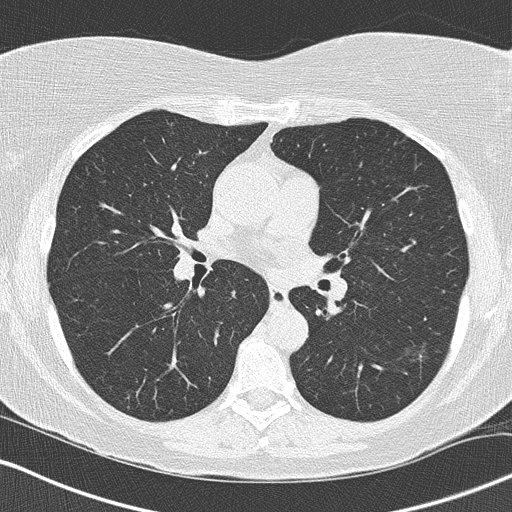
Low-dose screening chest CT, one axial slice; slice 82 of 160 in the series (ordered by position); reconstruction kernel B50f; 120 kVp; lung window (W 1500 / L -600 HU); 2 mm slice thickness; 512 × 512 image matrix, field of view 327 × 327 mm.
Structures marked on this image (outlined manually by an expert reader):
- lesion 1 (tumor, lower lobe of left lung): bounding box <406,343,430,363> (left, top, right, bottom; pixels)